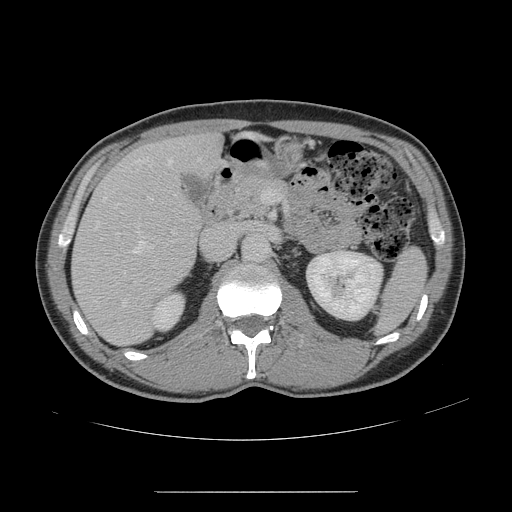
Contrast-enhanced abdominal CT, one axial slice; slice 78 of 178 in the series (ordered by position); 120 kVp; intravenous contrast given; soft-tissue window (W 400 / L 40 HU); 2.5 mm slice thickness; 512 × 512 image matrix, field of view 401 × 401 mm. Male patient, age 53 years. Case-level facts recorded for this patient, not image findings: diagnosis: colorectal cancer liver metastases, imaged before liver resection.
Structures marked on this image (manually delineated by an expert):
- hepatic veins: bounding box (x1, y1, x2, y2) in pixels: (96, 159, 172, 308)
- liver: (72, 134, 221, 345)
- planned liver remnant (the part of the liver to remain after resection): (165, 135, 221, 171)
- portal vein (with intrahepatic branches): (148, 190, 267, 203)